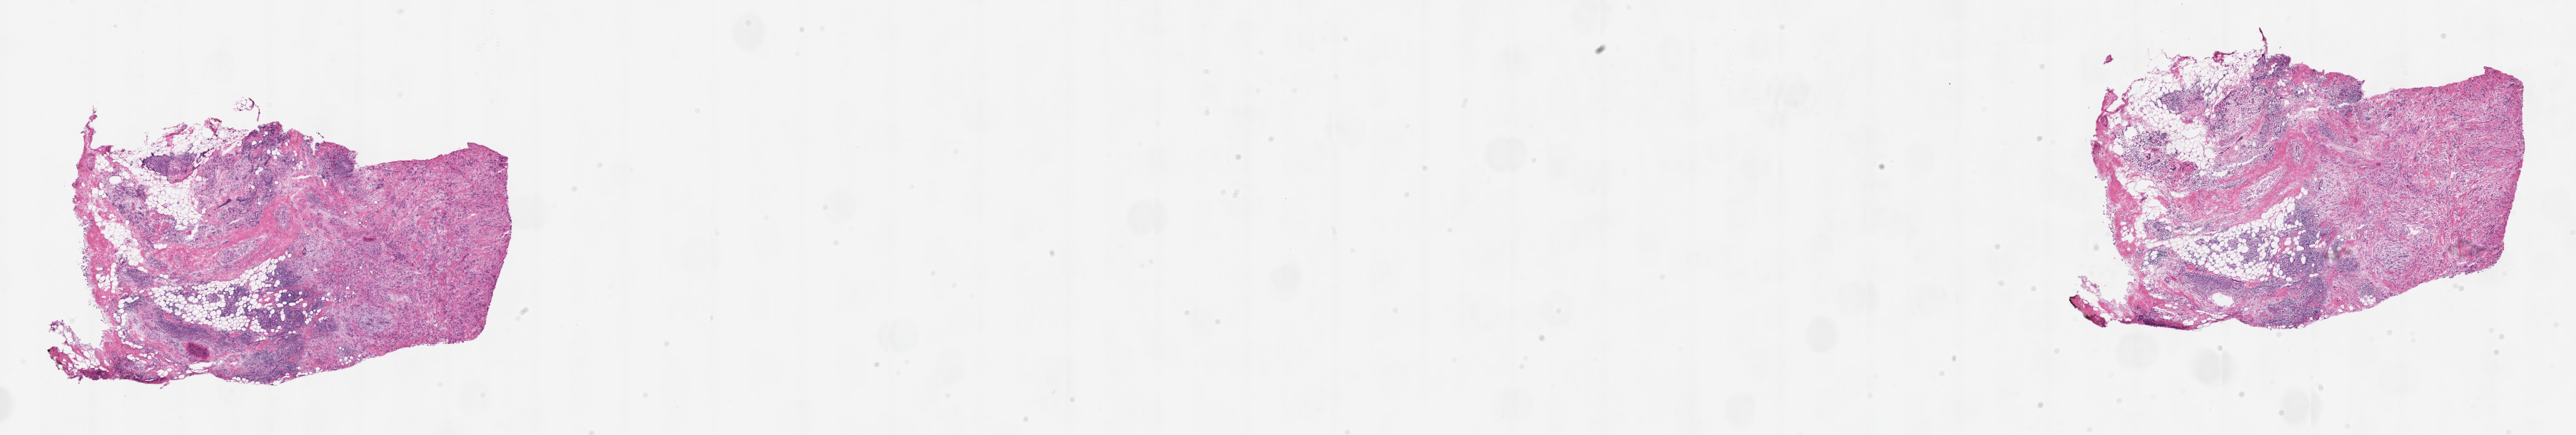
Whole-slide image, haematoxylin and eosin stain, a low-resolution overview of the entire scanned area, about 29.0 x 4.9 mm. Frozen section. Specimen: primary tumor. Anatomic site: breast (left). Patient: female, age at initial diagnosis 60 years. Pathologist review of this section (percent, as recorded): tumor cells 40%, tumor nuclei 40%, stromal cells 15%, necrosis 0%, normal cells 45%. Infiltration values recorded for this section: lymphocyte infiltration 20%, monocyte infiltration 2%, neutrophil infiltration 2%.
- histologic diagnosis: Infiltrating duct carcinoma, NOS
- section: top of the tissue portion